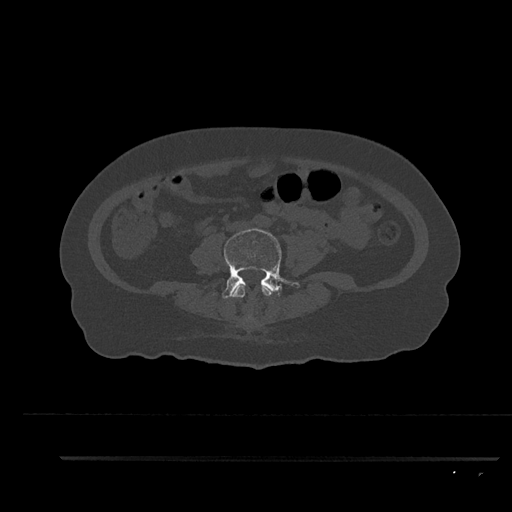
CT including the spine, one axial slice. Position 39 of 797 along the scan axis. Reconstruction kernel Br40s/3. Bone window (W 1800 / L 400 HU). 0.5 mm slice thickness. 512 × 512 image matrix. Female patient, age 44 years. From the clinical record (not read from this slice): primary cancer: renal.
Outlined on this slice (semi-automatic segmentation, software-assisted and operator-edited):
- L3 vertebra: bounding box (x1, y1, x2, y2) in pixels: (232, 284, 273, 320)
- L4 vertebra: (222, 228, 300, 299)